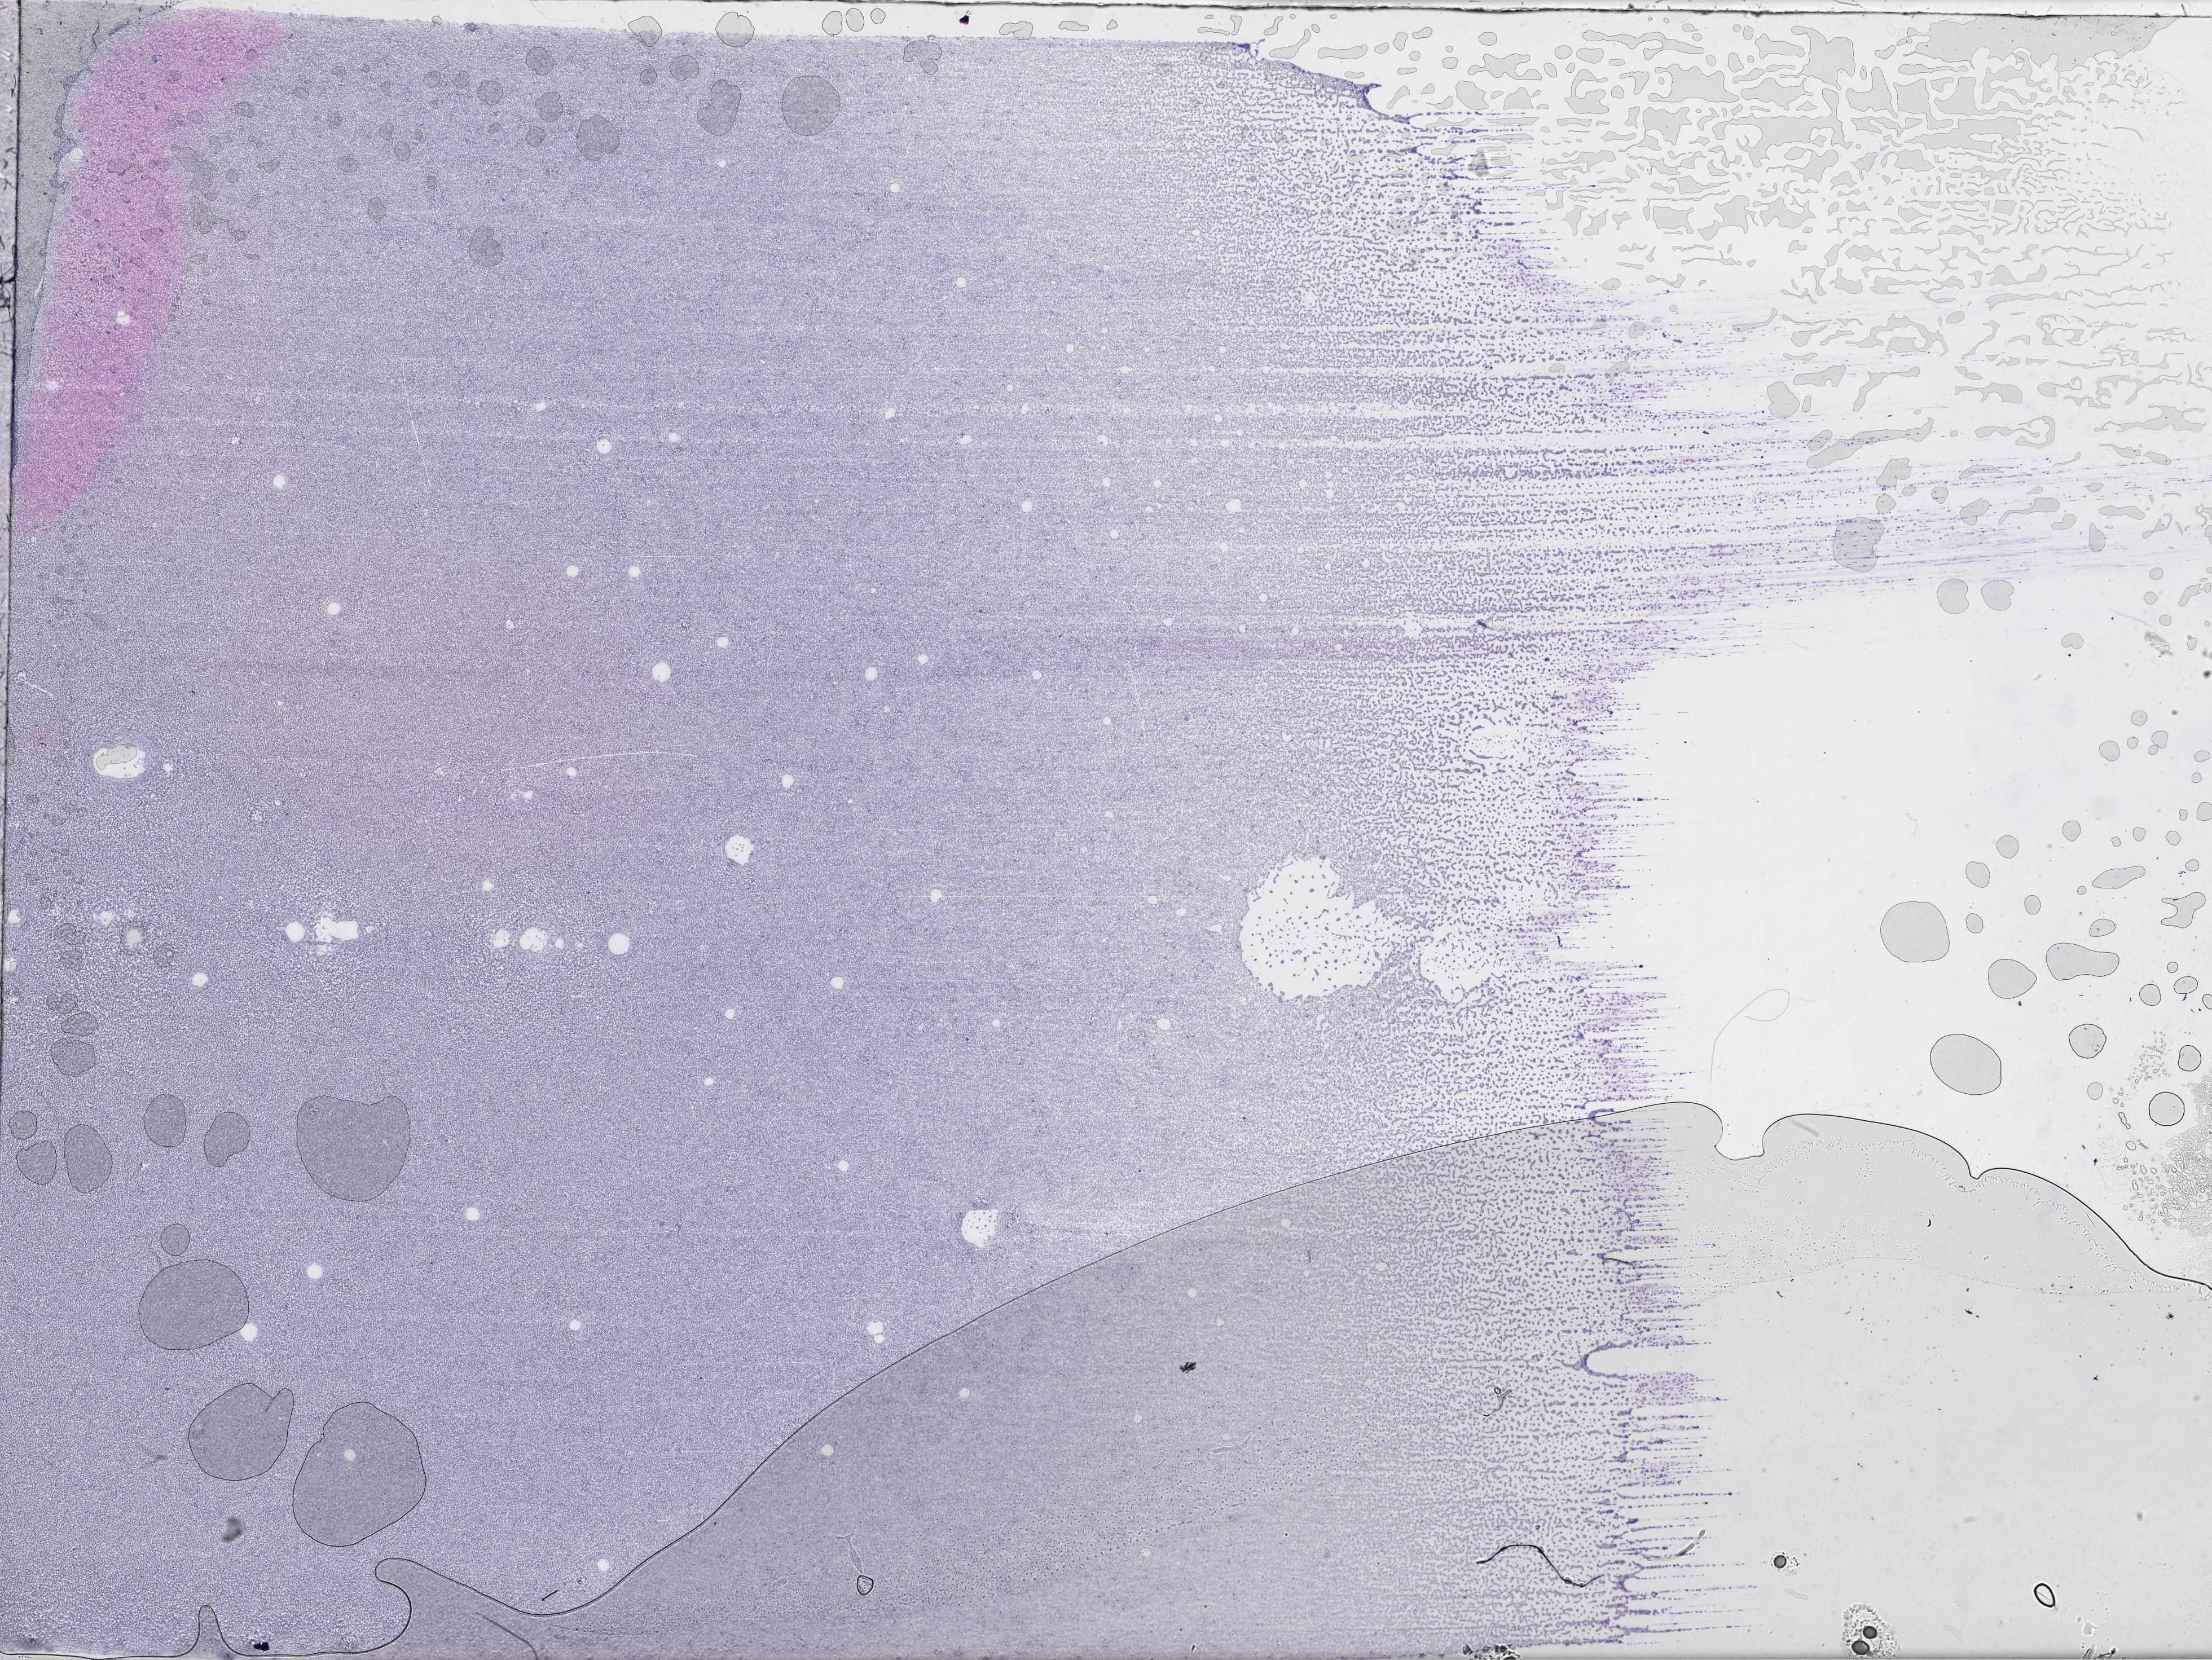
Digitized Hematoxylin and eosin (H&E) stained tissue section (whole slide) — low-resolution overview of the scanned area, about 31.7 x 23.8 mm (from a 40x scan); peripheral blood (leukaemic) sample. Patient: female, age 71 years.
FAB classification: M2. Diagnosis: Acute Myeloid Leukemia.